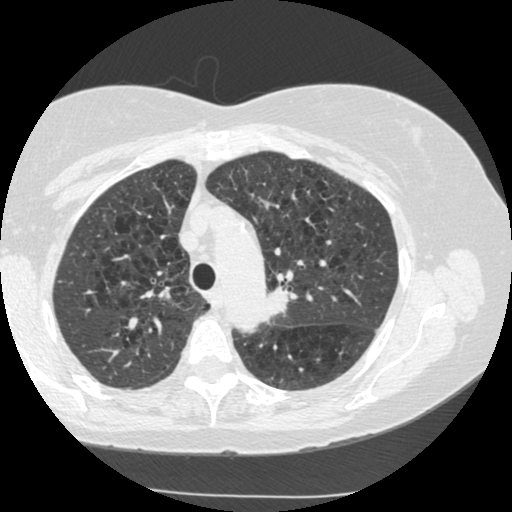
Low-dose screening chest CT, axial slice; second screening round (one year after baseline); lung window (W 1500 / L -600 HU); 1.25 mm slice thickness; slice 191 of 249 in the series. Female participant, aged 70 years at enrolment. Current smoker at enrolment.
Expert reader's lesion annotation, bounding box (x1, y1, x2, y2) in pixels: (242, 269, 307, 332). The exam's reader record, not a measurement of the box and not confirmed to be the same lesion: non-calcified nodule or mass ≥4 mm, left upper lobe, 15 × 13 mm, spiculated (stellate) margins, soft tissue attenuation, pre-existing on the prior screen: yes; interval growth: yes. Later outcome: lung cancer diagnosed 360 days after this screen (after the third annual screen) — neoplasm, malignant, left upper lobe, stage IIIB (AJCC 6th edition), 40 mm at pathology.